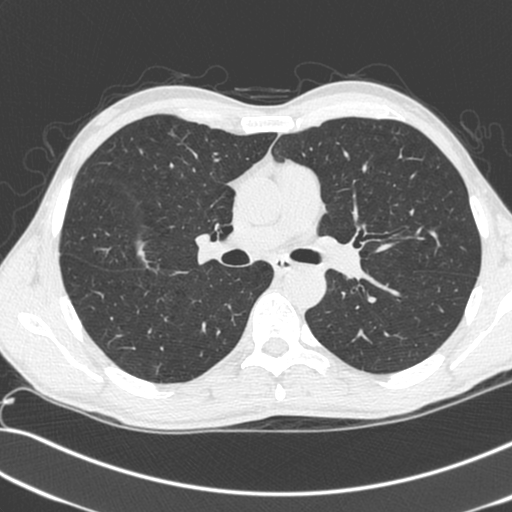
Low-dose screening chest CT, axial slice, baseline screening round, lung window (W 1500 / L -600 HU), 1.3 mm slice thickness, 120 kVp, 512 × 512 image matrix. Male, age 55 years at enrolment.
- Expert reader's lesion annotation, bounding box (x1, y1, x2, y2) in pixels: (64, 212, 160, 293).
- Screening reader's record for this exam (one nodule recorded; not confirmed to be the boxed lesion): non-calcified nodule or mass ≥4 mm, right upper lobe, 52 × 39 mm, spiculated (stellate) margins, soft tissue attenuation.
- Official screen result: positive, change unspecified: nodule(s) >= 4 mm or enlarging nodule(s), mass(es), or other non-specific abnormalities suspicious for lung cancer.
- Lung cancer was diagnosed 25 days after this screen: large cell neuroendocrine carcinoma, right upper lobe, poorly differentiated (G3), stage IIB (AJCC 6th edition), 49 mm at pathology.